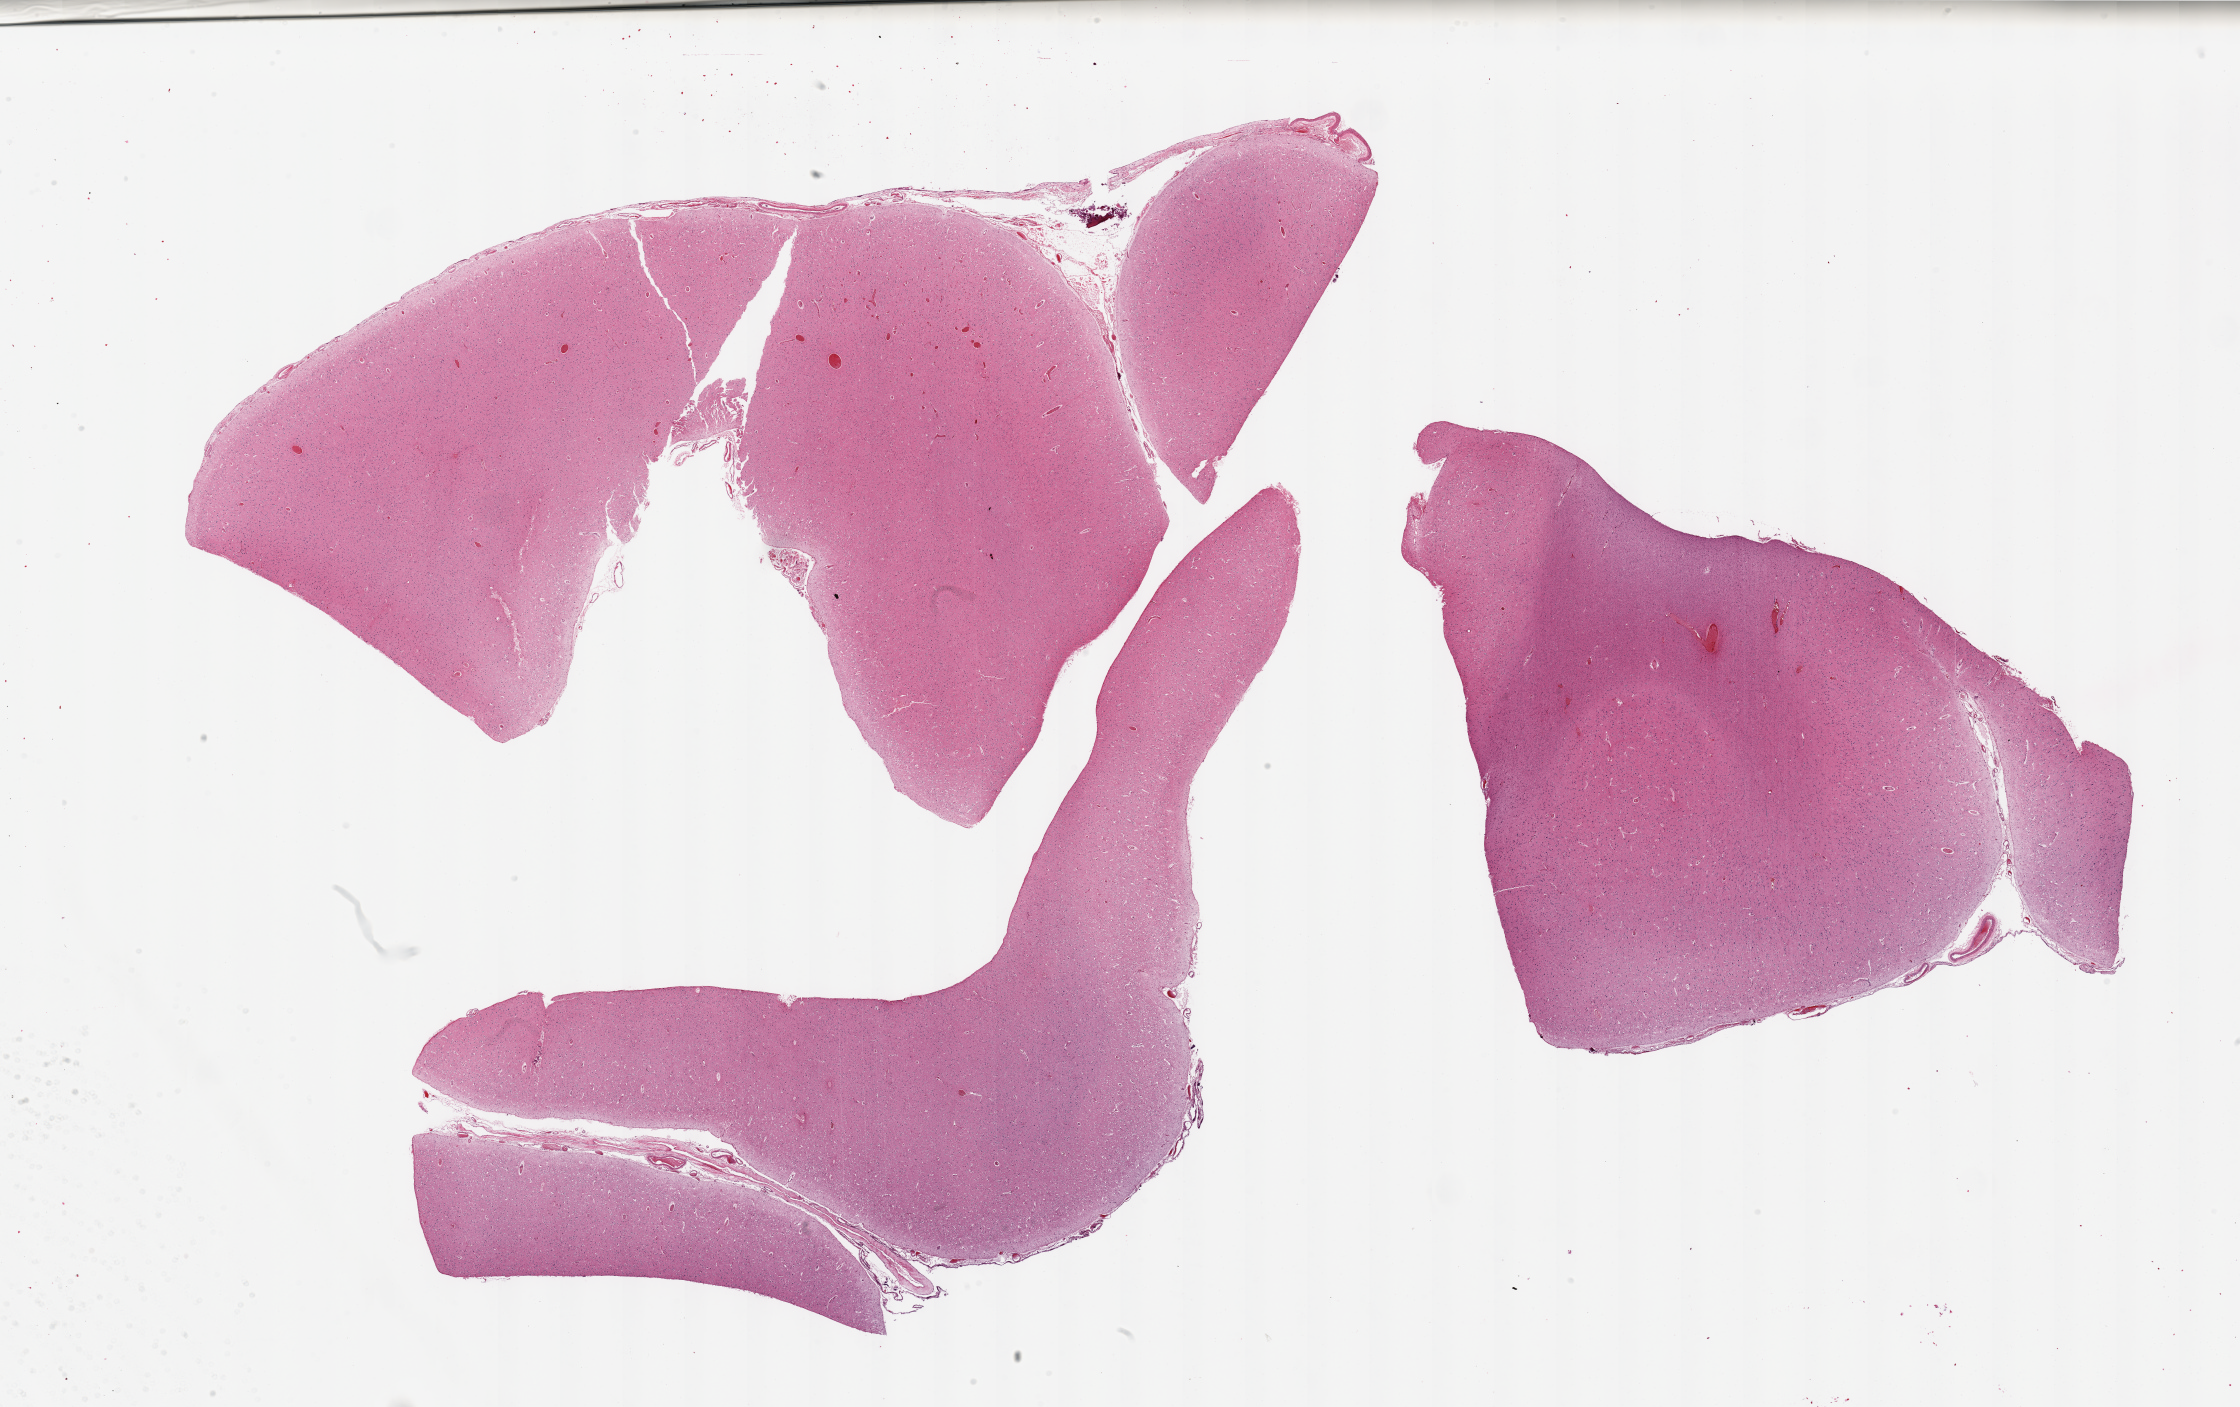
Hematoxylin and eosin (H&E) whole-slide image — whole scanned area (about 35.4 x 22.3 mm) shown as a low-resolution overview. PAXgene-fixed paraffin-embedded (PFPE) section. Sampled site (target tissue): cerebral cortex. Donor tissue sample. Male donor.
* review note (as recorded): 3 pieces; some residual attached meninges